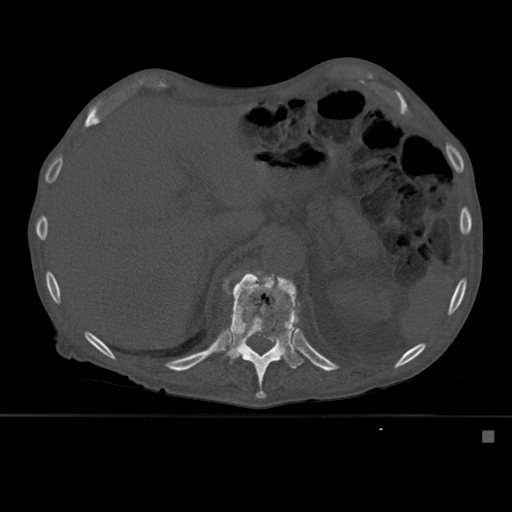
CT including the spine, one axial slice. Slice 276 of 527 in the series (ordered by position). Bone window (W 1800 / L 400 HU). 1.5 mm slice thickness. 512 × 512 image matrix. Male patient, age 78 years. Case-level facts recorded for this patient, not image findings: primary cancer: prostate.
Outlined on this slice (semi-automatic segmentation, software-assisted and operator-edited):
- T12 vertebra: bounding box <224,271,303,399> (left, top, right, bottom; pixels)